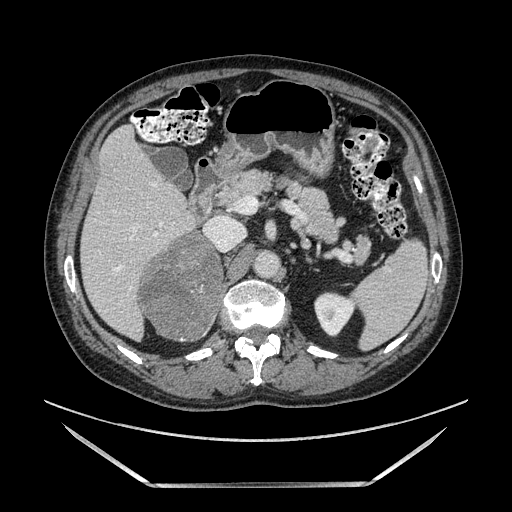
Contrast-enhanced abdominal CT, one axial slice; position 80 of 185 along the scan axis; soft-tissue window (W 400 / L 40 HU); 1.25 mm slice thickness; 512 × 512 image matrix. Male patient. Case-level facts recorded for this patient, not image findings: diagnosis: adrenocortical carcinoma; tumour side: right adrenal; tumour size at pathology: 10.3 cm.
Outlined on this slice (semi-automatic segmentation, software-assisted and operator-edited):
- mass: bounding box <142,235,218,339> (left, top, right, bottom; pixels)